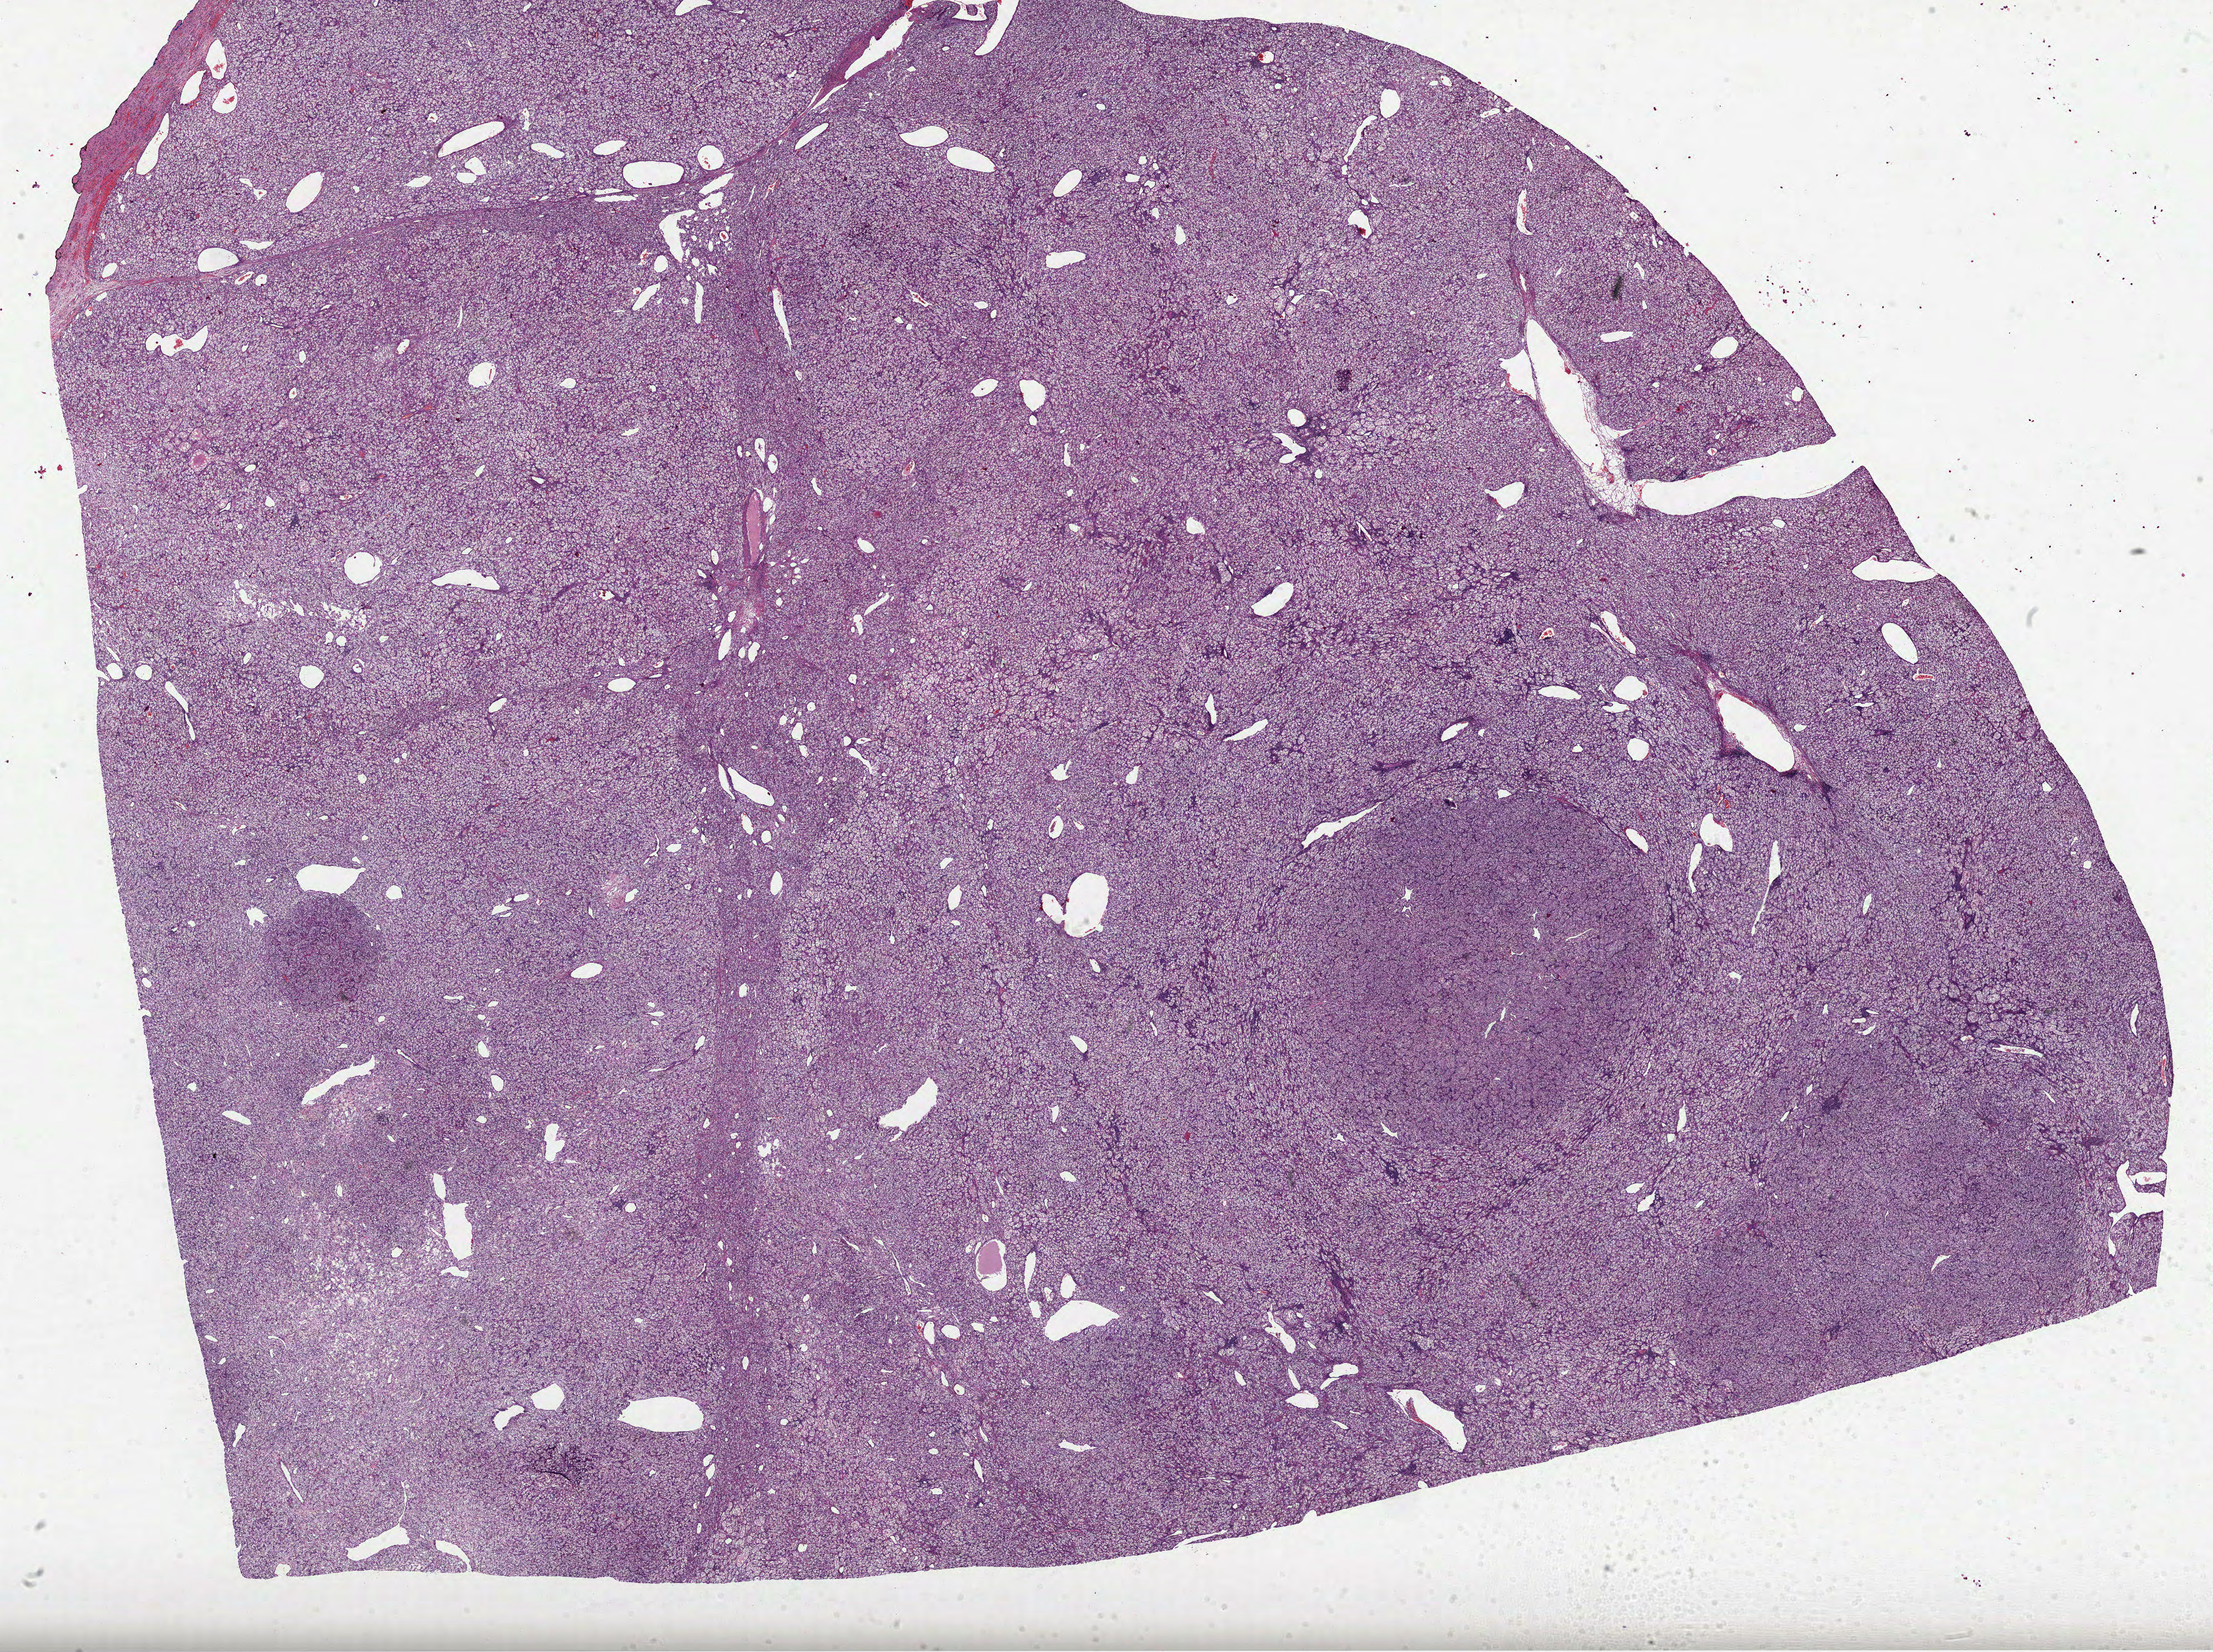
Whole-slide histology image, Hematoxylin and eosin (H&E) stained — a low-resolution overview of the entire scanned area, about 28.5 x 21.3 mm (acquisition: 40x scan); formalin-fixed paraffin-embedded (FFPE) diagnostic section; sample: primary tumour, kidney. Patient: male, age at initial diagnosis 46 years. Histologic grade: G2 (moderately differentiated).
AJCC pathologic stage: I. Diagnosis: Clear cell adenocarcinoma, NOS. TNM: T1b N0 M0.